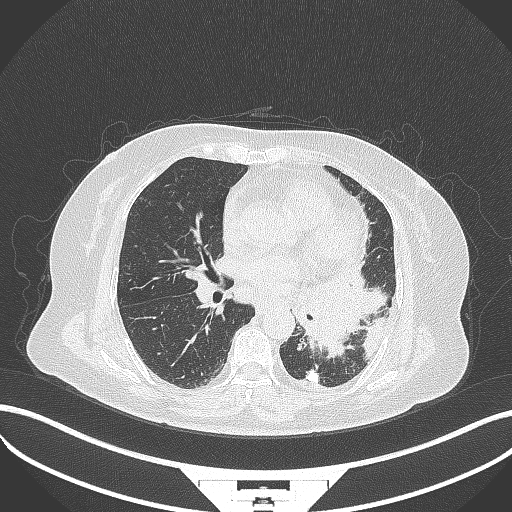
Chest CT, one axial slice; slice 169 of 322 in the series (ordered by position); reconstruction kernel B70f; lung window (W 1500 / L -600 HU); 1 mm slice thickness; 512 × 512 image matrix. Female patient, age 69 years. From the clinical record (not read from this slice): clinical TNM (as recorded): T2b N3 M1.
Annotated regions visible in this slice (bounding box drawn by a radiologist):
- lung tumour (recorded histology: adenocarcinoma): box from (x=292, y=269) to (x=384, y=354) px